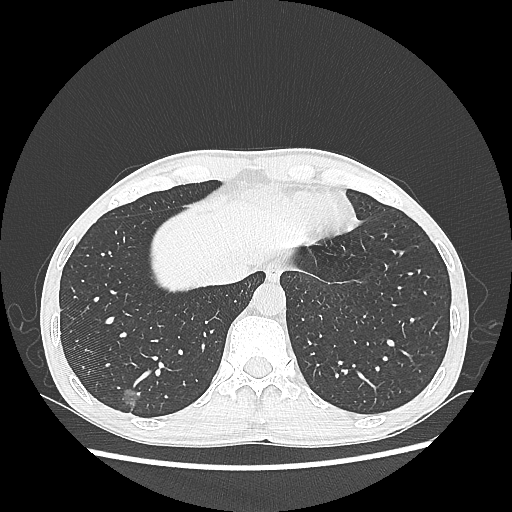
Chest CT, one axial slice; position 63 of 270 along the scan axis; lung window (W 1500 / L -600 HU); 1.25 mm slice thickness; 512 × 512 image matrix. Male patient, age 60 years. From the clinical record (not read from this slice): clinical TNM (as recorded): T1c N0 M0; histopathological grade: G2.
Structures marked on this image (rectangle marked by the reading radiologist):
- lung tumour (recorded histology: adenocarcinoma): bounding box [x1, y1, x2, y2] px = [114, 382, 142, 415]